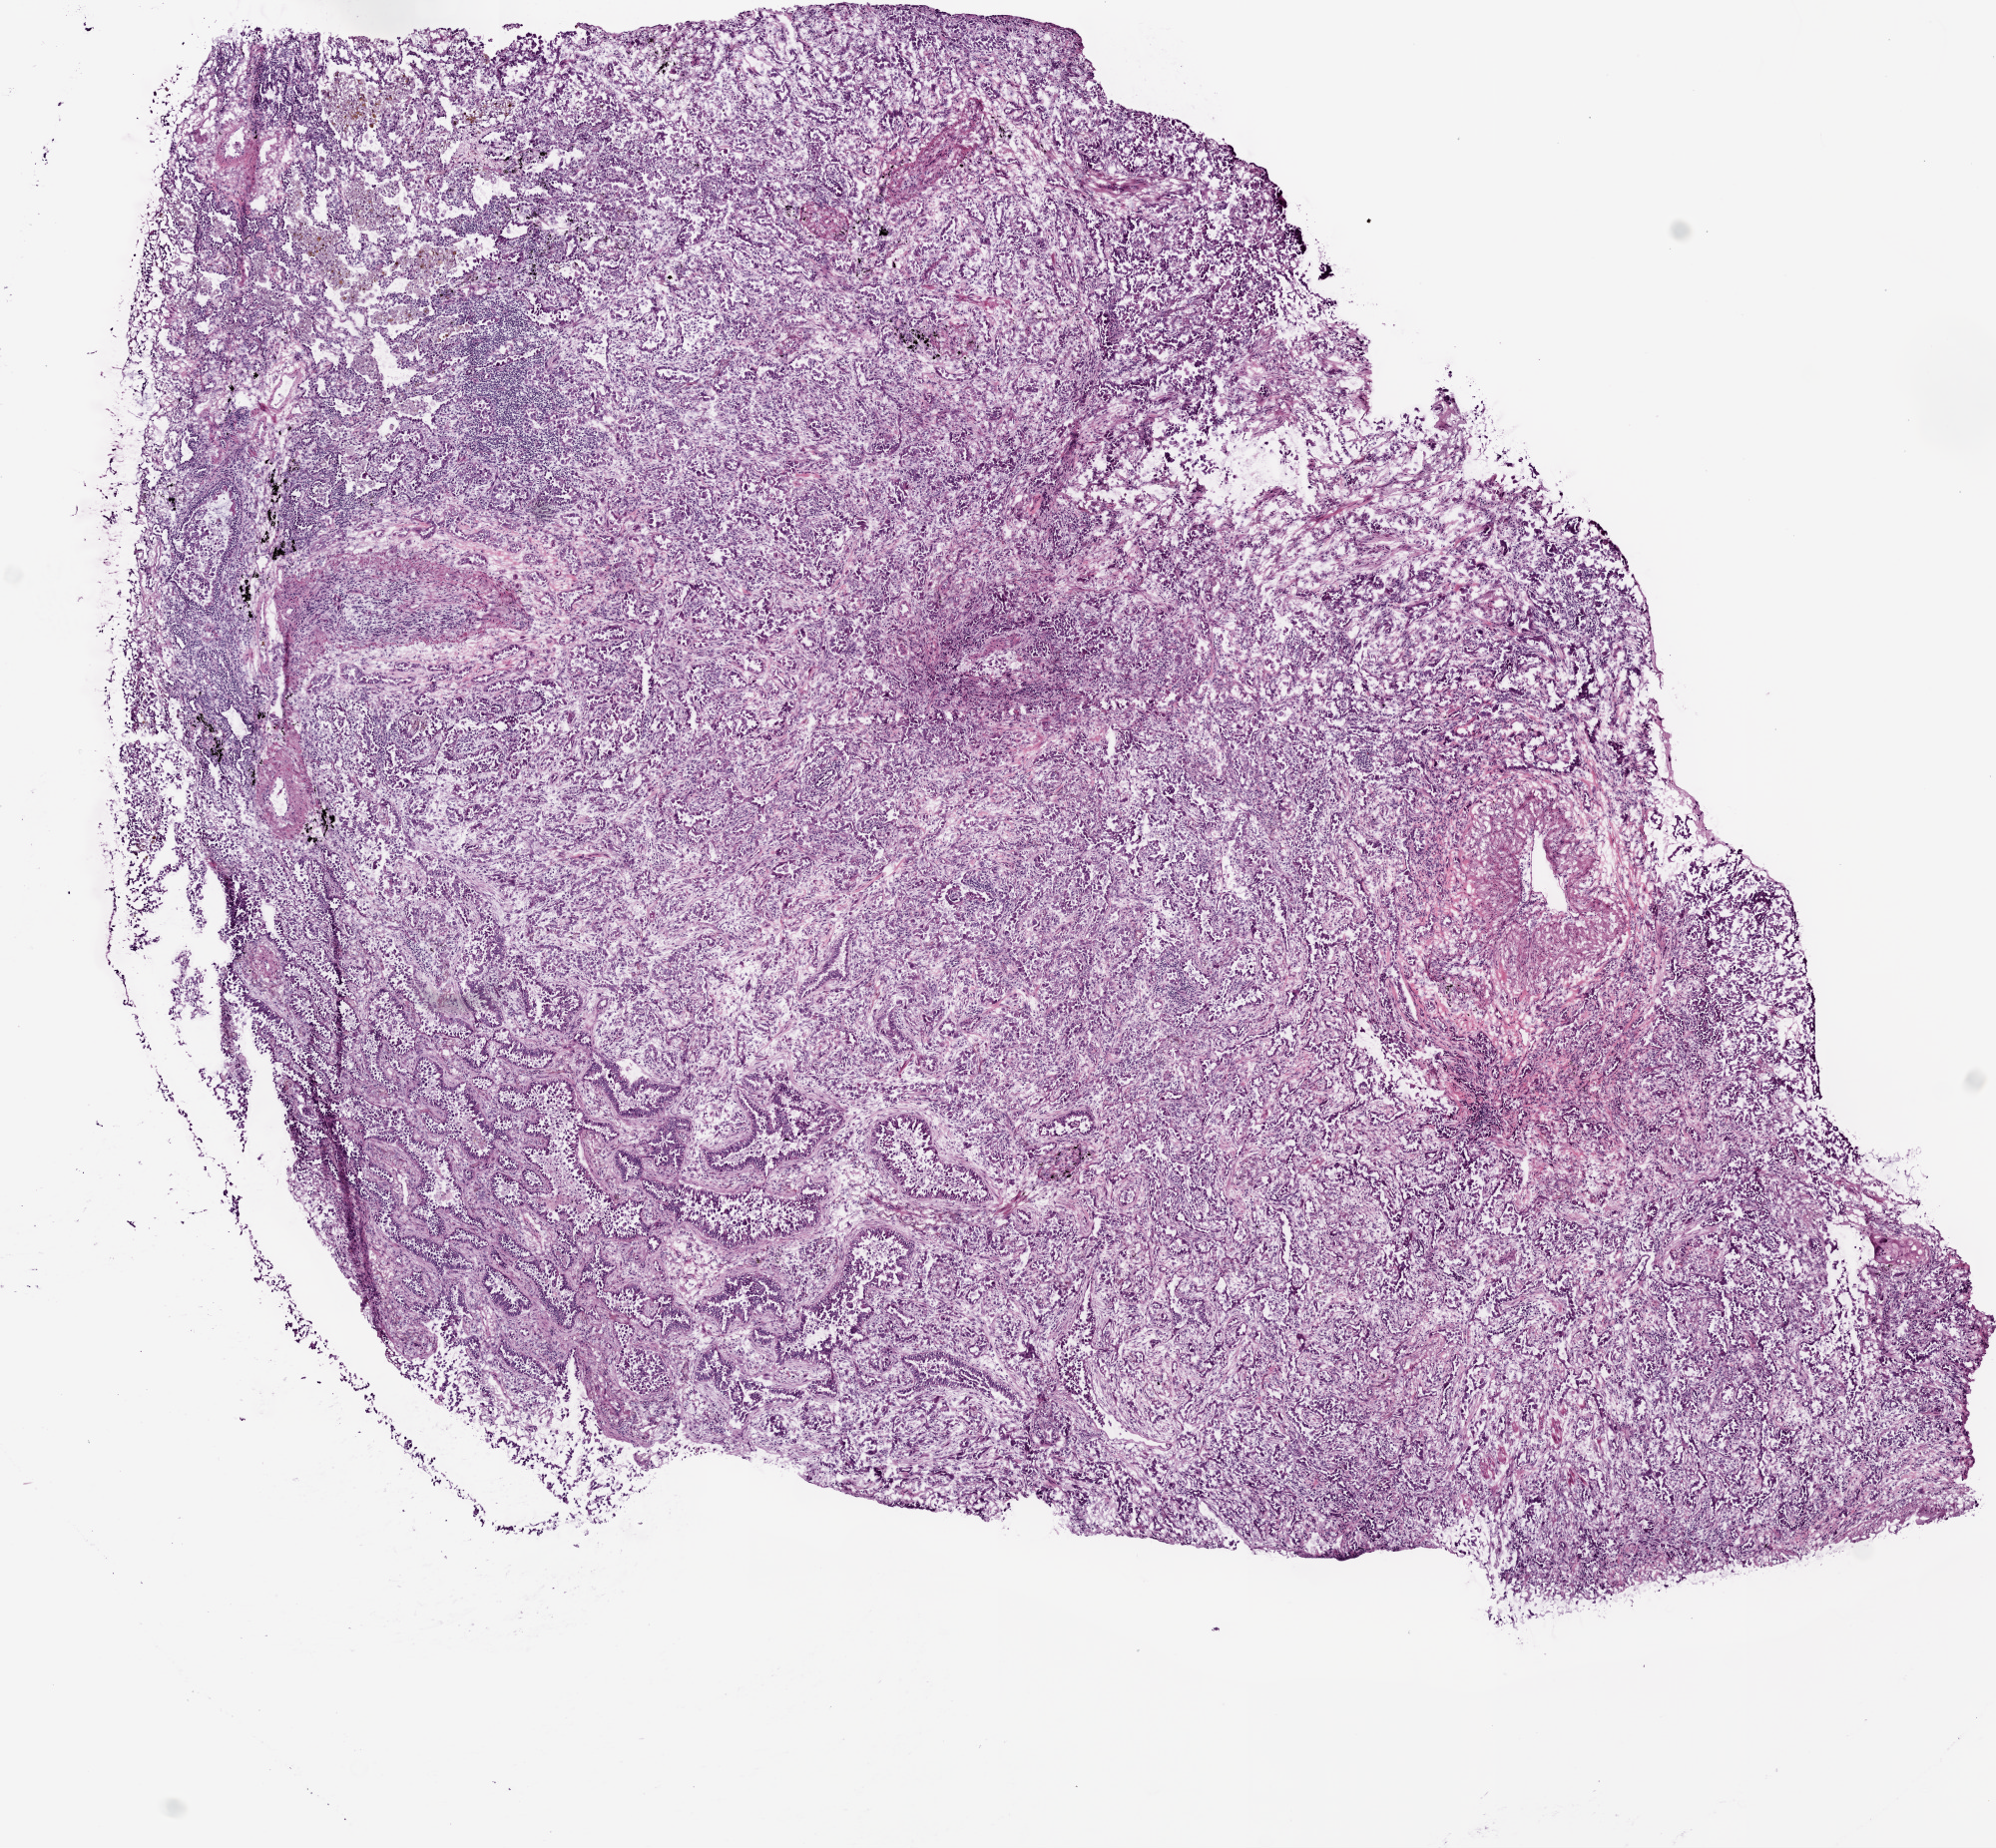
Whole-slide histology image, H&E-stained — shown as a low-resolution overview of the whole scanned area (about 8.0 x 7.4 mm, acquisition: 20x scan). Frozen section from the bottom of the tissue portion. Sample: primary tumour, lung. Female patient; age at initial diagnosis 74 years. Slide review estimates, as recorded: tumour cells 70%, tumour nuclei 65%, normal cells 10%, stromal cells 20%, necrosis 0%.
• AJCC pathologic stage: IB (5th edition)
• diagnosis: Adenocarcinoma with mixed subtypes (lower lobe, lung)
• laterality: right